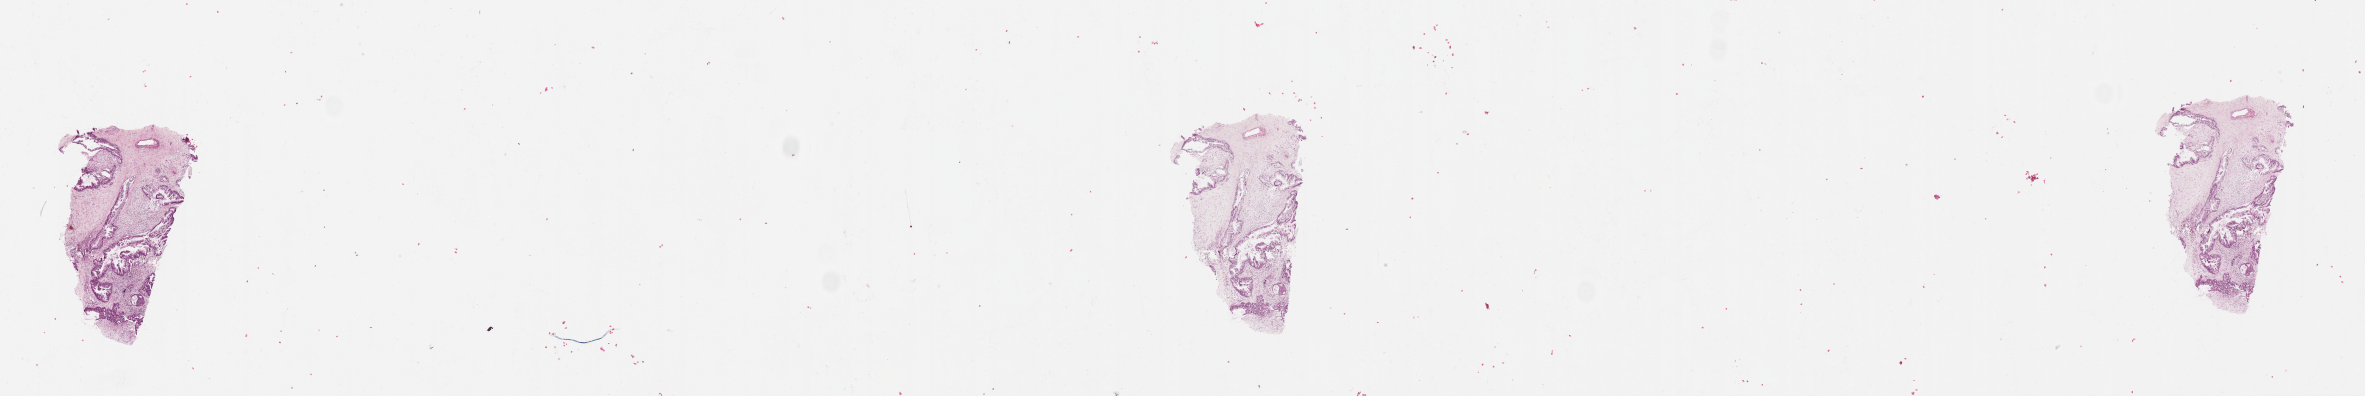
H&E whole-slide image — shown as a low-resolution overview of the whole scanned area (about 38.1 x 6.4 mm); tumour tissue sample, sampled site: pancreas. Patient: female, age 69 years.
Diagnosis: Infiltrating duct carcinoma, NOS.